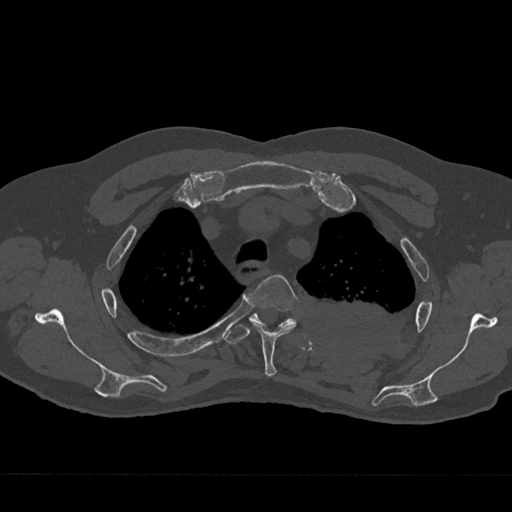
CT including the spine, one axial slice. Position 549 of 797 along the scan axis. Reconstruction kernel Br40s/3. Bone window (W 1800 / L 400 HU). 0.5 mm slice thickness. 512 × 512 image matrix, field of view 377 × 377 mm. Patient: male, 75 years. From the clinical record (not read from this slice): primary cancer: renal; vertebrae with lytic lesions (as recorded): T4.
Structures marked on this image (semi-automatic segmentation, software-assisted and operator-edited):
- T3 vertebra: box from (x=249, y=275) to (x=300, y=377) px
- T4 vertebra: (x=225, y=313)–(x=297, y=344)